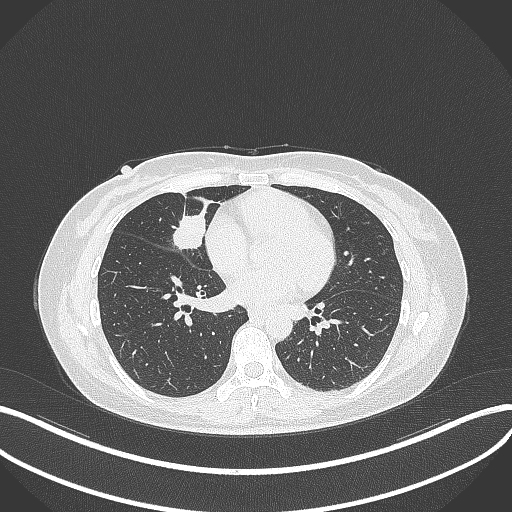
Chest CT, one axial slice; slice 124 of 284 in the series (ordered by position); reconstruction kernel B70f; 120 kVp; lung window (W 1500 / L -600 HU); 512 × 512 image matrix, field of view 400 × 400 mm. Female patient, age 43 years. Case-level facts recorded for this patient, not image findings: clinical TNM (as recorded): T1c N3 M1.
Outlined on this slice (rectangle marked by the reading radiologist):
- lung tumour (recorded histology: adenocarcinoma): bounding box (x1, y1, x2, y2) in pixels: (166, 200, 212, 253)